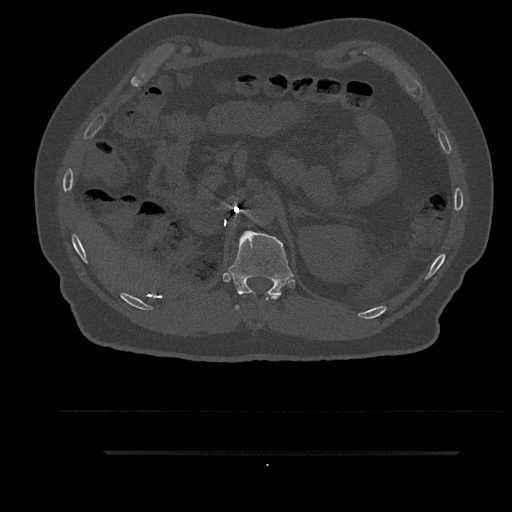
CT including the spine, one axial slice. Position 259 of 797 along the scan axis. Bone window (W 1800 / L 400 HU). 512 × 512 image matrix. Male patient, age 63 years. Case-level facts recorded for this patient, not image findings: primary cancer: renal.
Annotated regions visible in this slice (semi-automatic segmentation, software-assisted and operator-edited):
- T11 vertebra: box from (x=244, y=294) to (x=279, y=300) px
- T12 vertebra: (x=226, y=230)–(x=294, y=310)